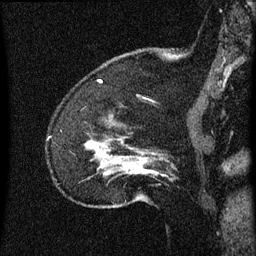
Breast MRI (dynamic contrast-enhanced), one sagittal slice. Slice 12 of 60 in the series (ordered by position). Dynamic contrast-enhanced series, image 2 of 3 at this slice position (ordered by acquisition). 1.5 T. TE 4.2 ms, TR 8 ms. 256 × 256 image matrix. Patient: female, 52 years.
Structures marked on this image (semi-automatically segmented with operator editing):
- analysis volume of interest (the breast-tissue region the enhancement analysis was run in; not a lesion): bounding box (x1, y1, x2, y2) in pixels: (85, 116, 156, 207)
- tumour enhancement mask (voxels above the 70 % enhancement threshold inside the analysis volume of interest): (88, 142, 155, 175)